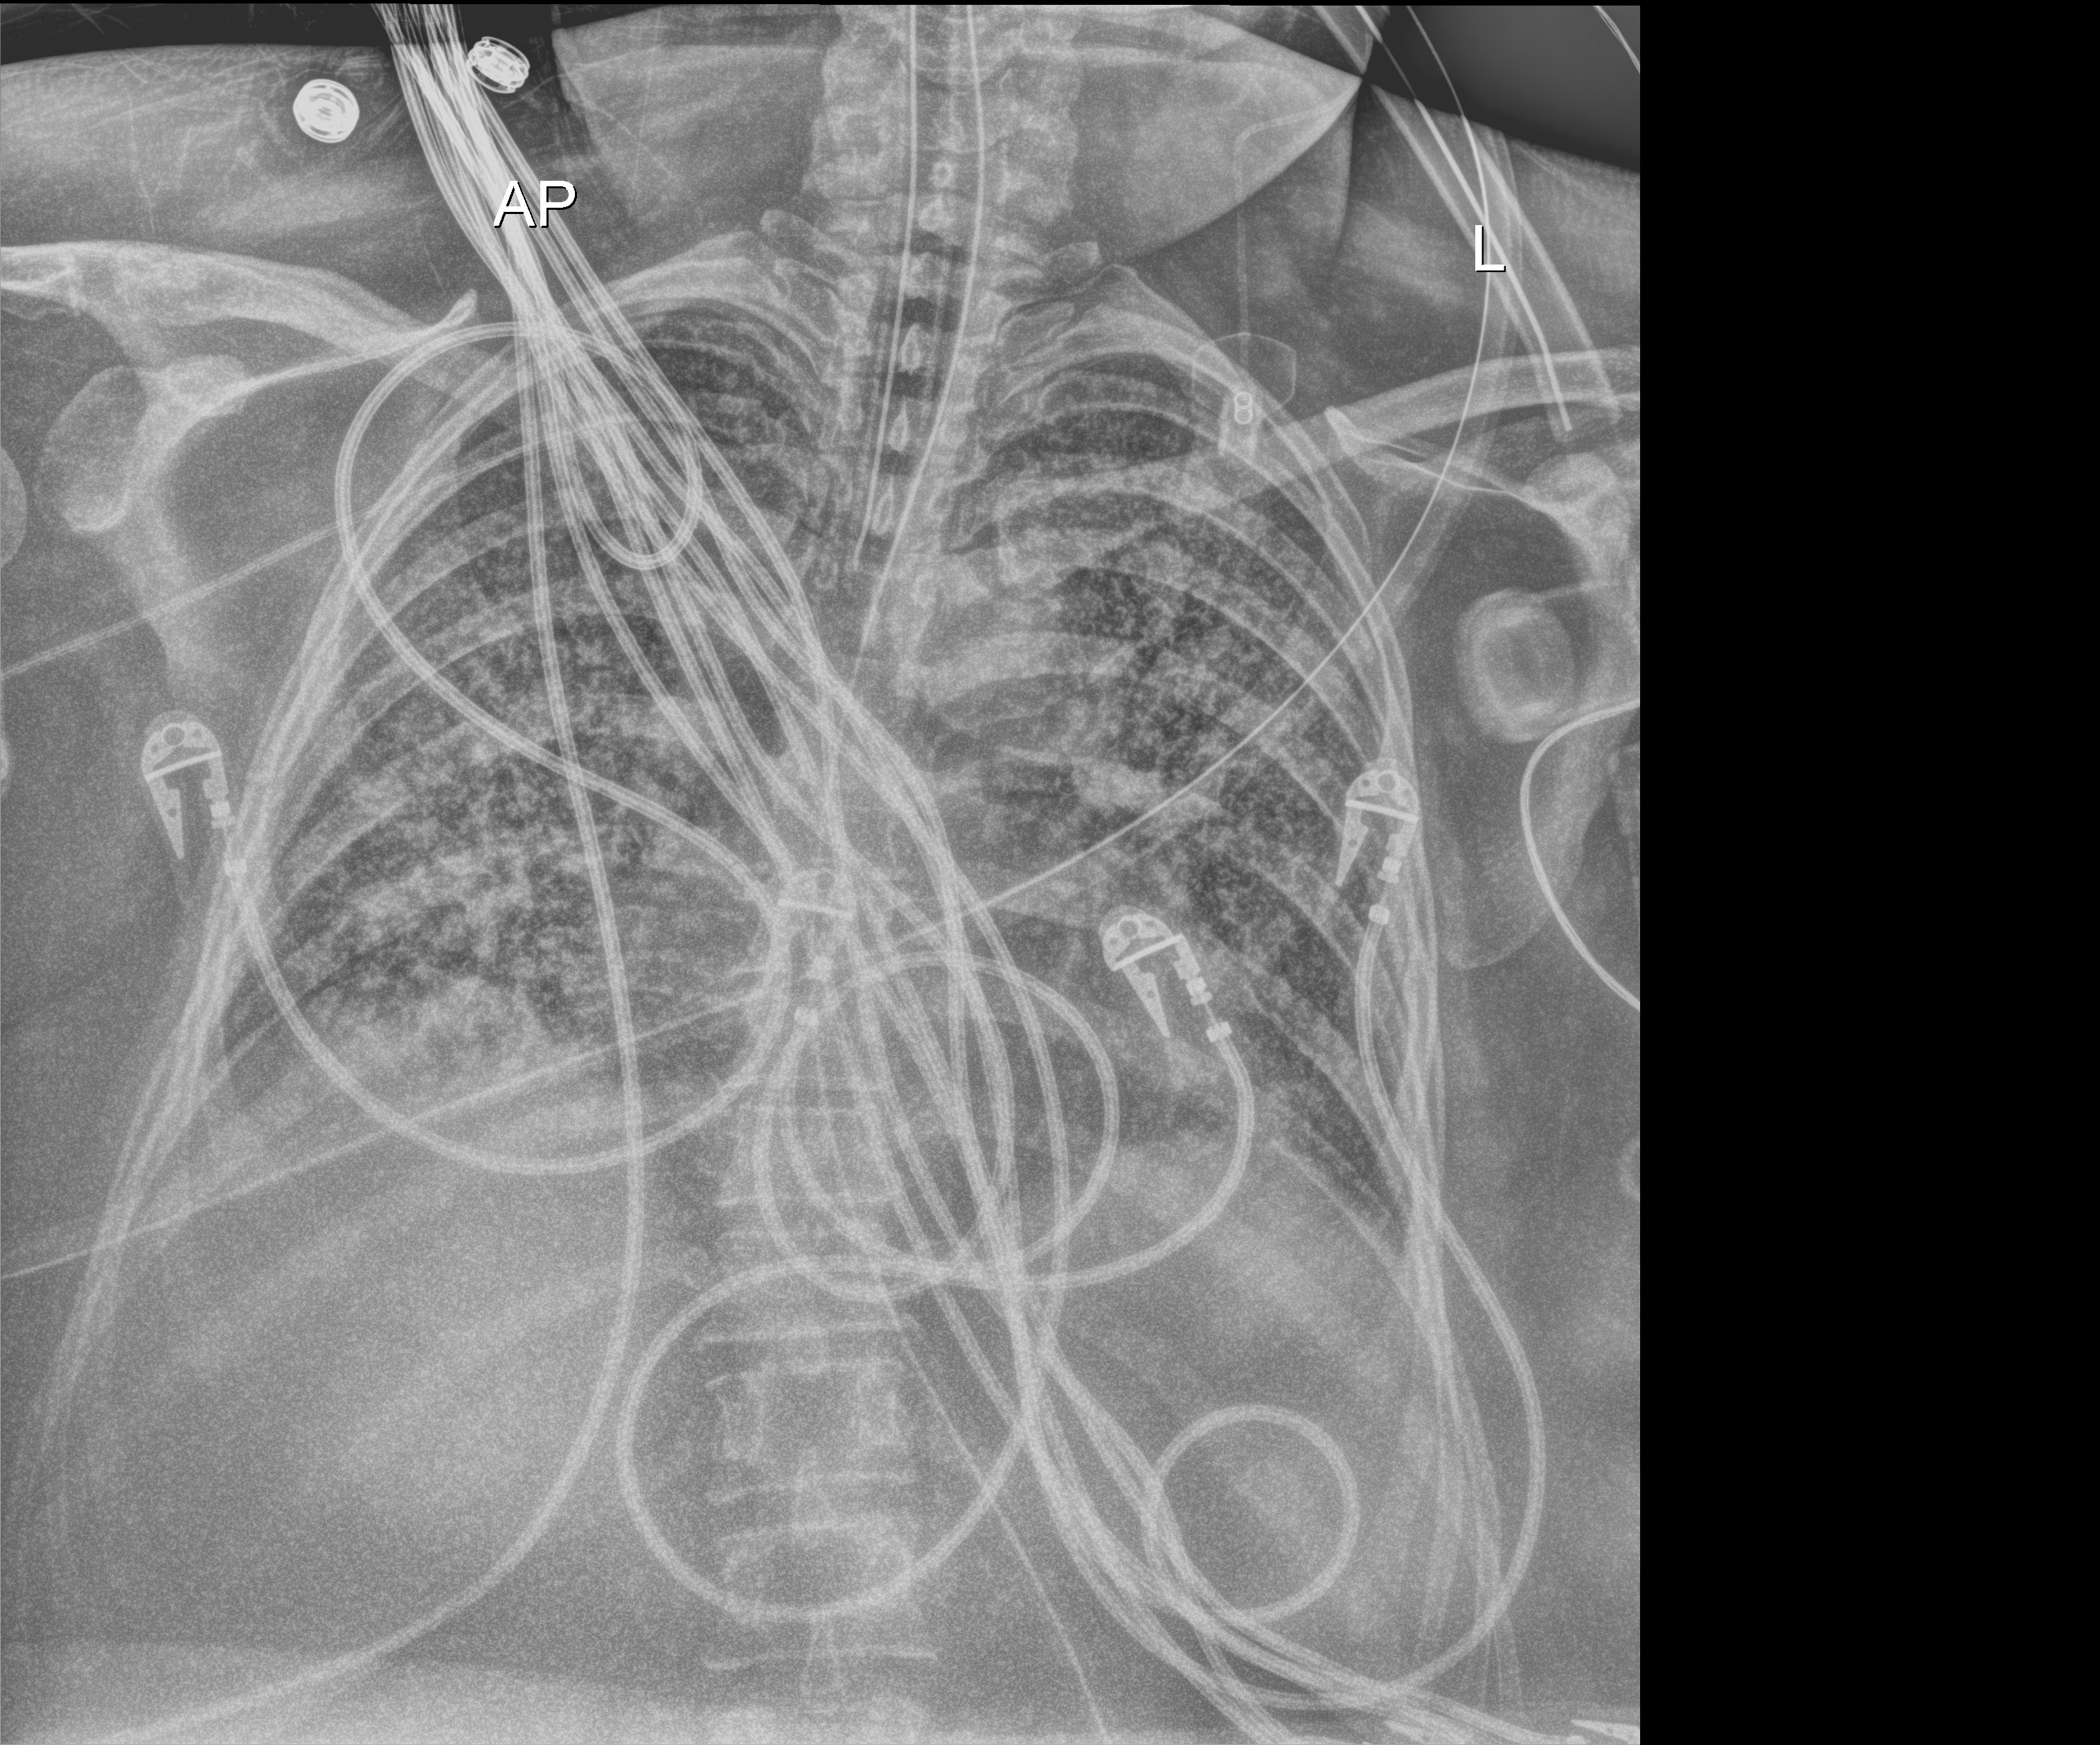
Chest X-ray (portable); anteroposterior (AP) projection. Female patient hospitalised with COVID-19, age 18–59 years.
From the hospital-stay record, not from the radiograph (when in the stay this image was taken is not recorded): admitted to intensive care during this hospital stay: yes.